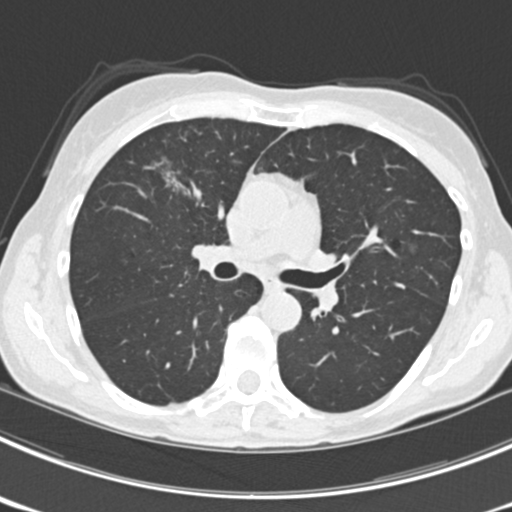
Chest CT (low-dose screening protocol), one axial image. Third annual screen. Lung window (W 1500 / L -600 HU). 2 mm slice thickness. Standard (soft-tissue) reconstruction kernel (B30f). 120 kVp. Slice 85 of 225 in the series. 512 × 512 image matrix. Female, age 63 years at enrolment. Current smoker at enrolment.
Lesion marked by an expert reader, bounding box [x1, y1, x2, y2] px = [147, 150, 208, 205]. The screening reader recorded 9 non-calcified nodules or masses ≥4 mm on this exam (left upper lobe, right upper lobe, left upper lobe, left lower lobe, right middle lobe, left lower lobe, left lower lobe, right lower lobe, right lower lobe); which of them this box marks is not recorded. Official screen result: positive, other.